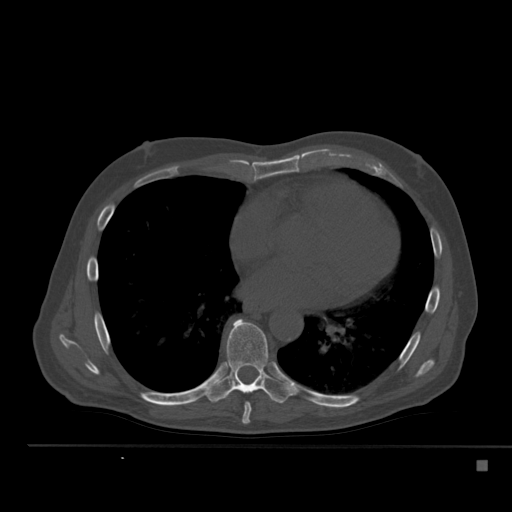
CT including the spine, one axial slice; position 312 of 517 along the scan axis; reconstruction kernel Br40s; 120 kVp; bone window (W 1800 / L 400 HU); 1.5 mm slice thickness; 512 × 512 image matrix. Patient: male, 70 years. Case-level facts recorded for this patient, not image findings: primary cancer: renal; vertebrae with lytic lesions (as recorded): T4, T6, T10, T12, L3, L4, L5.
Outlined on this slice (semi-automatic segmentation, software-assisted and operator-edited):
- T7 vertebra: bounding box [x1, y1, x2, y2] px = [242, 403, 251, 424]
- T8 vertebra: [205, 319, 289, 403]